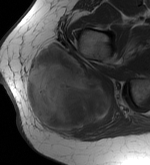
MRI of an extremity soft-tissue mass, one axial slice. Slice 25 of 56 in the series (ordered by position). MR volume resampled by the dataset authors to the PET/CT grid (not the native acquisition matrix). 3.27 mm slice thickness. 150 × 165 image matrix, field of view 146 × 161 mm. Female patient. From the clinical record (not read from this slice): histological type: epithelioid sarcoma with vascular differentiation; site of the primary tumour: right buttock.
Outlined on this slice (expert contour drawn on MRI and transferred to this co-registered scan by the dataset authors):
- gross tumour volume (mass): bounding box [x1, y1, x2, y2] px = [25, 42, 115, 137]